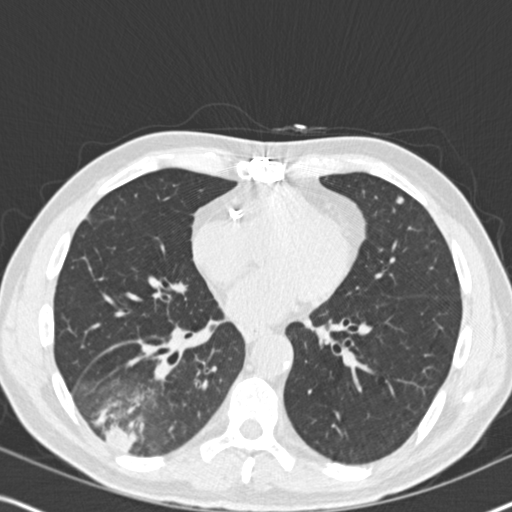
Axial slice from a low-dose chest CT screening exam, second screening round (one year after baseline), lung window (W 1500 / L -600 HU), 512 × 512 image matrix. Male, age 61 years at enrolment. Current smoker at enrolment.
• Lesion marked by an expert reader, bounding box (x1, y1, x2, y2) in pixels: (62, 344, 193, 468).
• Reader record for this screening exam (exam-level; its link to the box is not recorded): non-calcified nodule or mass ≥4 mm, right lower lobe, 90 × 80 mm, soft tissue attenuation, pre-existing on the prior screen: yes; interval growth: yes.
• Lung cancer was diagnosed 20 days after this screen: bronchiolo-alveolar adenocarcinoma, NOS, right lower lobe, moderately differentiated (G2), stage IIIB (AJCC 6th edition), 90 mm at pathology.